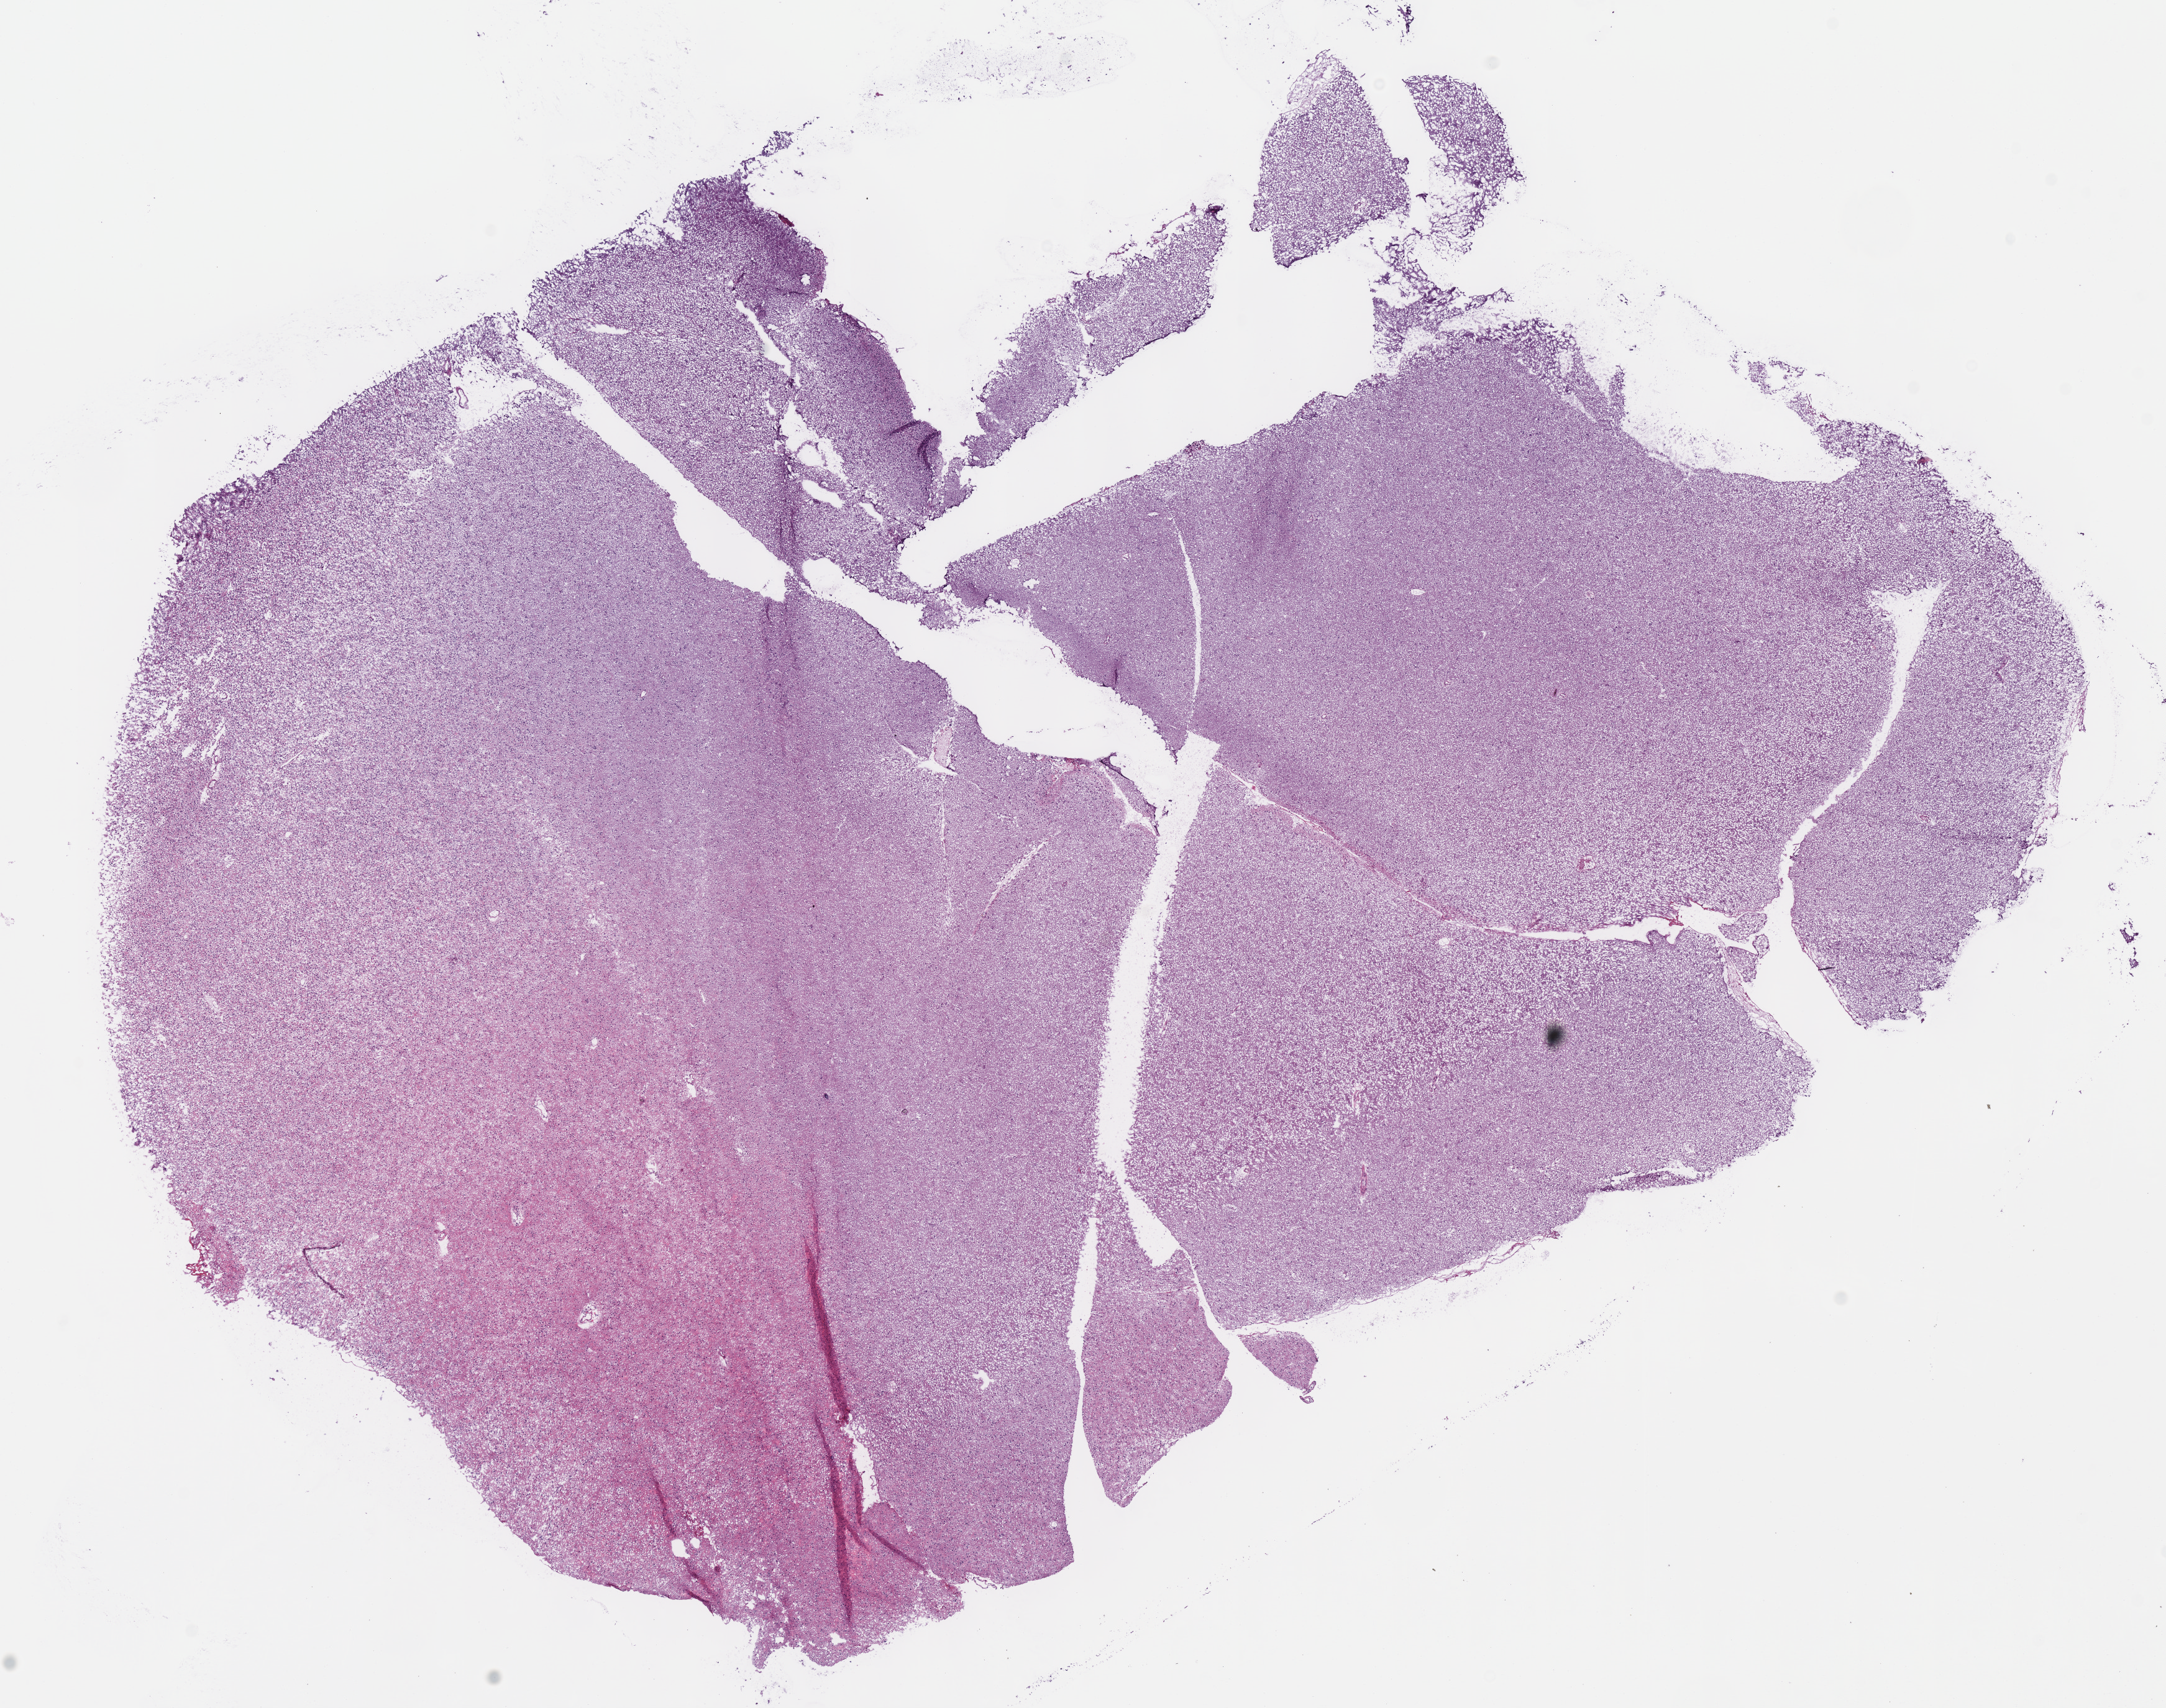
Whole-slide histology image, H&E-stained — low-resolution overview of the scanned area, about 13.7 x 10.8 mm. Frozen section from the bottom of the tissue portion. Primary tumour sample from the brain. Female, age 29 years at initial diagnosis. Histologic grade: G2 (moderately differentiated). Slide review estimates, as recorded: tumour cells 100%, tumour nuclei 50%, normal cells 0%, stromal cells 0%, necrosis 0%.
Laterality: left. Pathologic diagnosis: Oligodendroglioma, NOS (cerebrum).